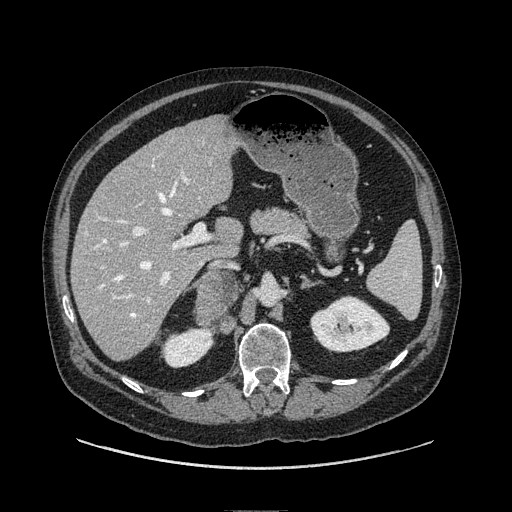
Contrast-enhanced abdominal CT, one axial slice. Slice 50 of 149 in the series (ordered by position). Soft-tissue window (W 400 / L 40 HU). 512 × 512 image matrix. Male patient. From the clinical record (not read from this slice): diagnosis: adrenocortical carcinoma; tumour side: right adrenal; tumour size at pathology: 7.5 cm; Ki-67 index: 15 %; stage (as recorded): 2.
Annotated regions visible in this slice (semi-automatically segmented with operator editing):
- mass: bounding box [x1, y1, x2, y2] px = [195, 273, 240, 322]